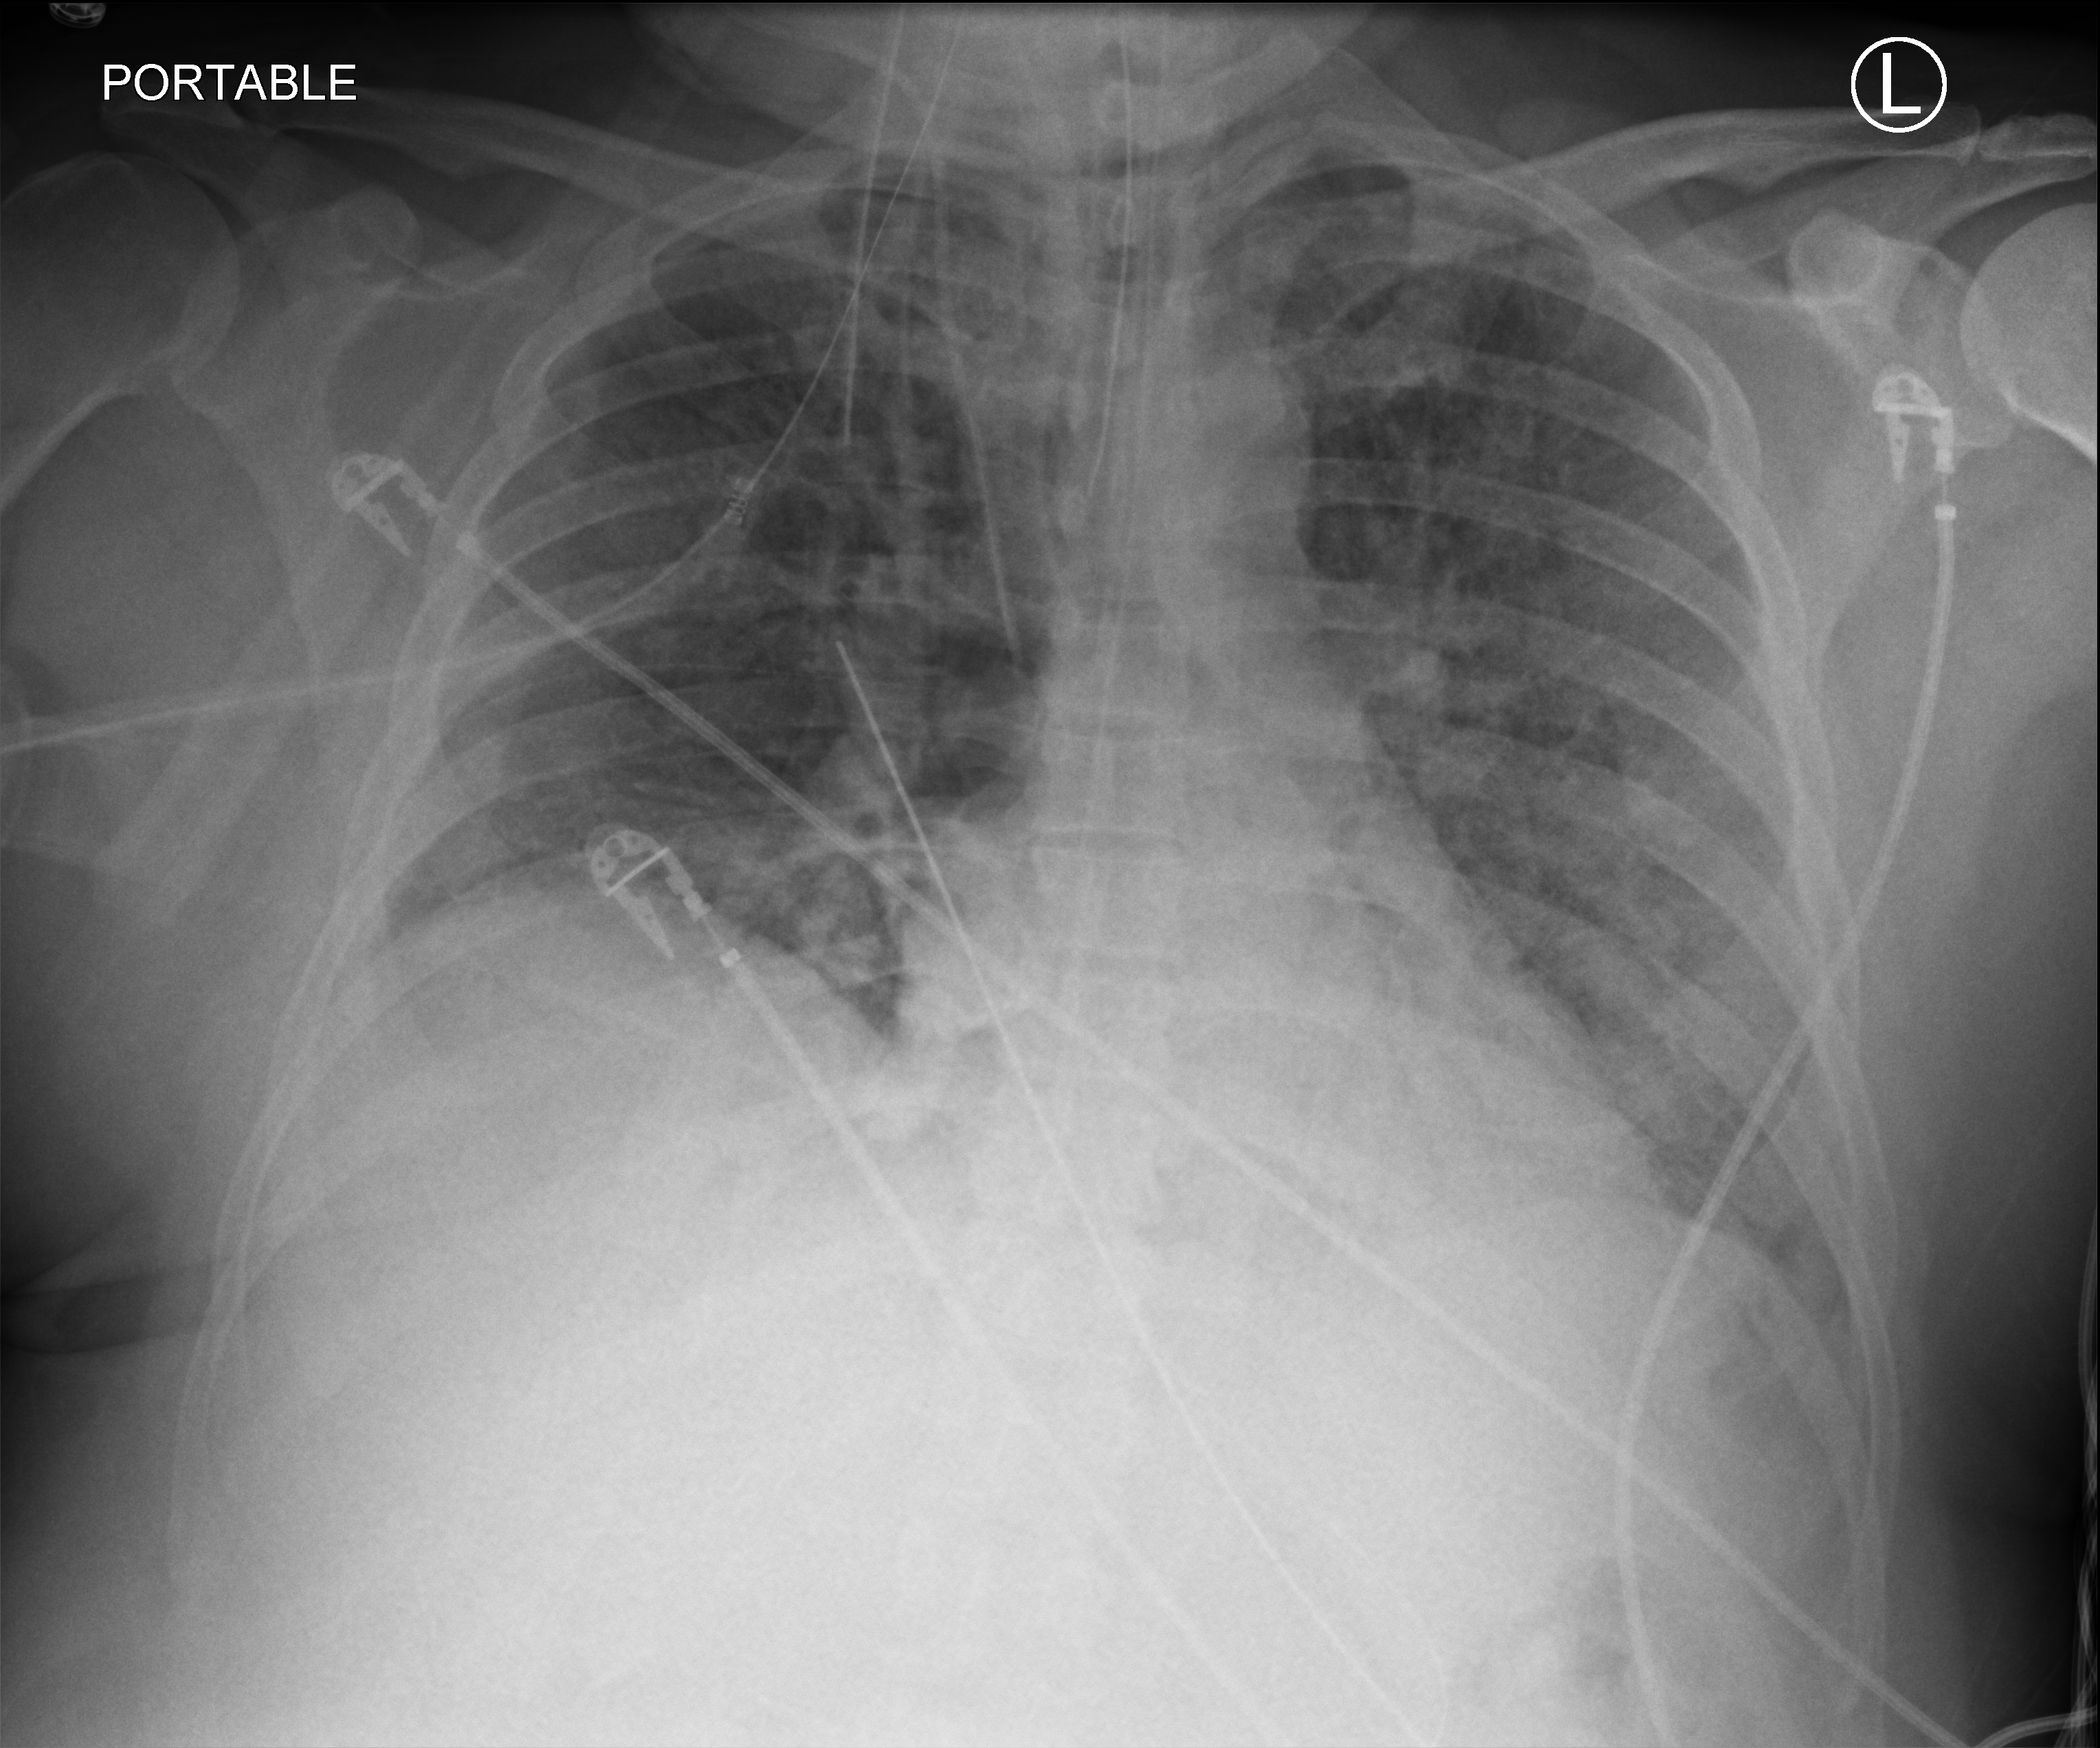
Portable chest radiograph, anteroposterior (AP) projection. Male patient hospitalised with COVID-19, age 18–59 years.
Hospital-stay facts (about this admission, not read from this image; timing relative to this image not recorded):
- smoking status (admission record): never